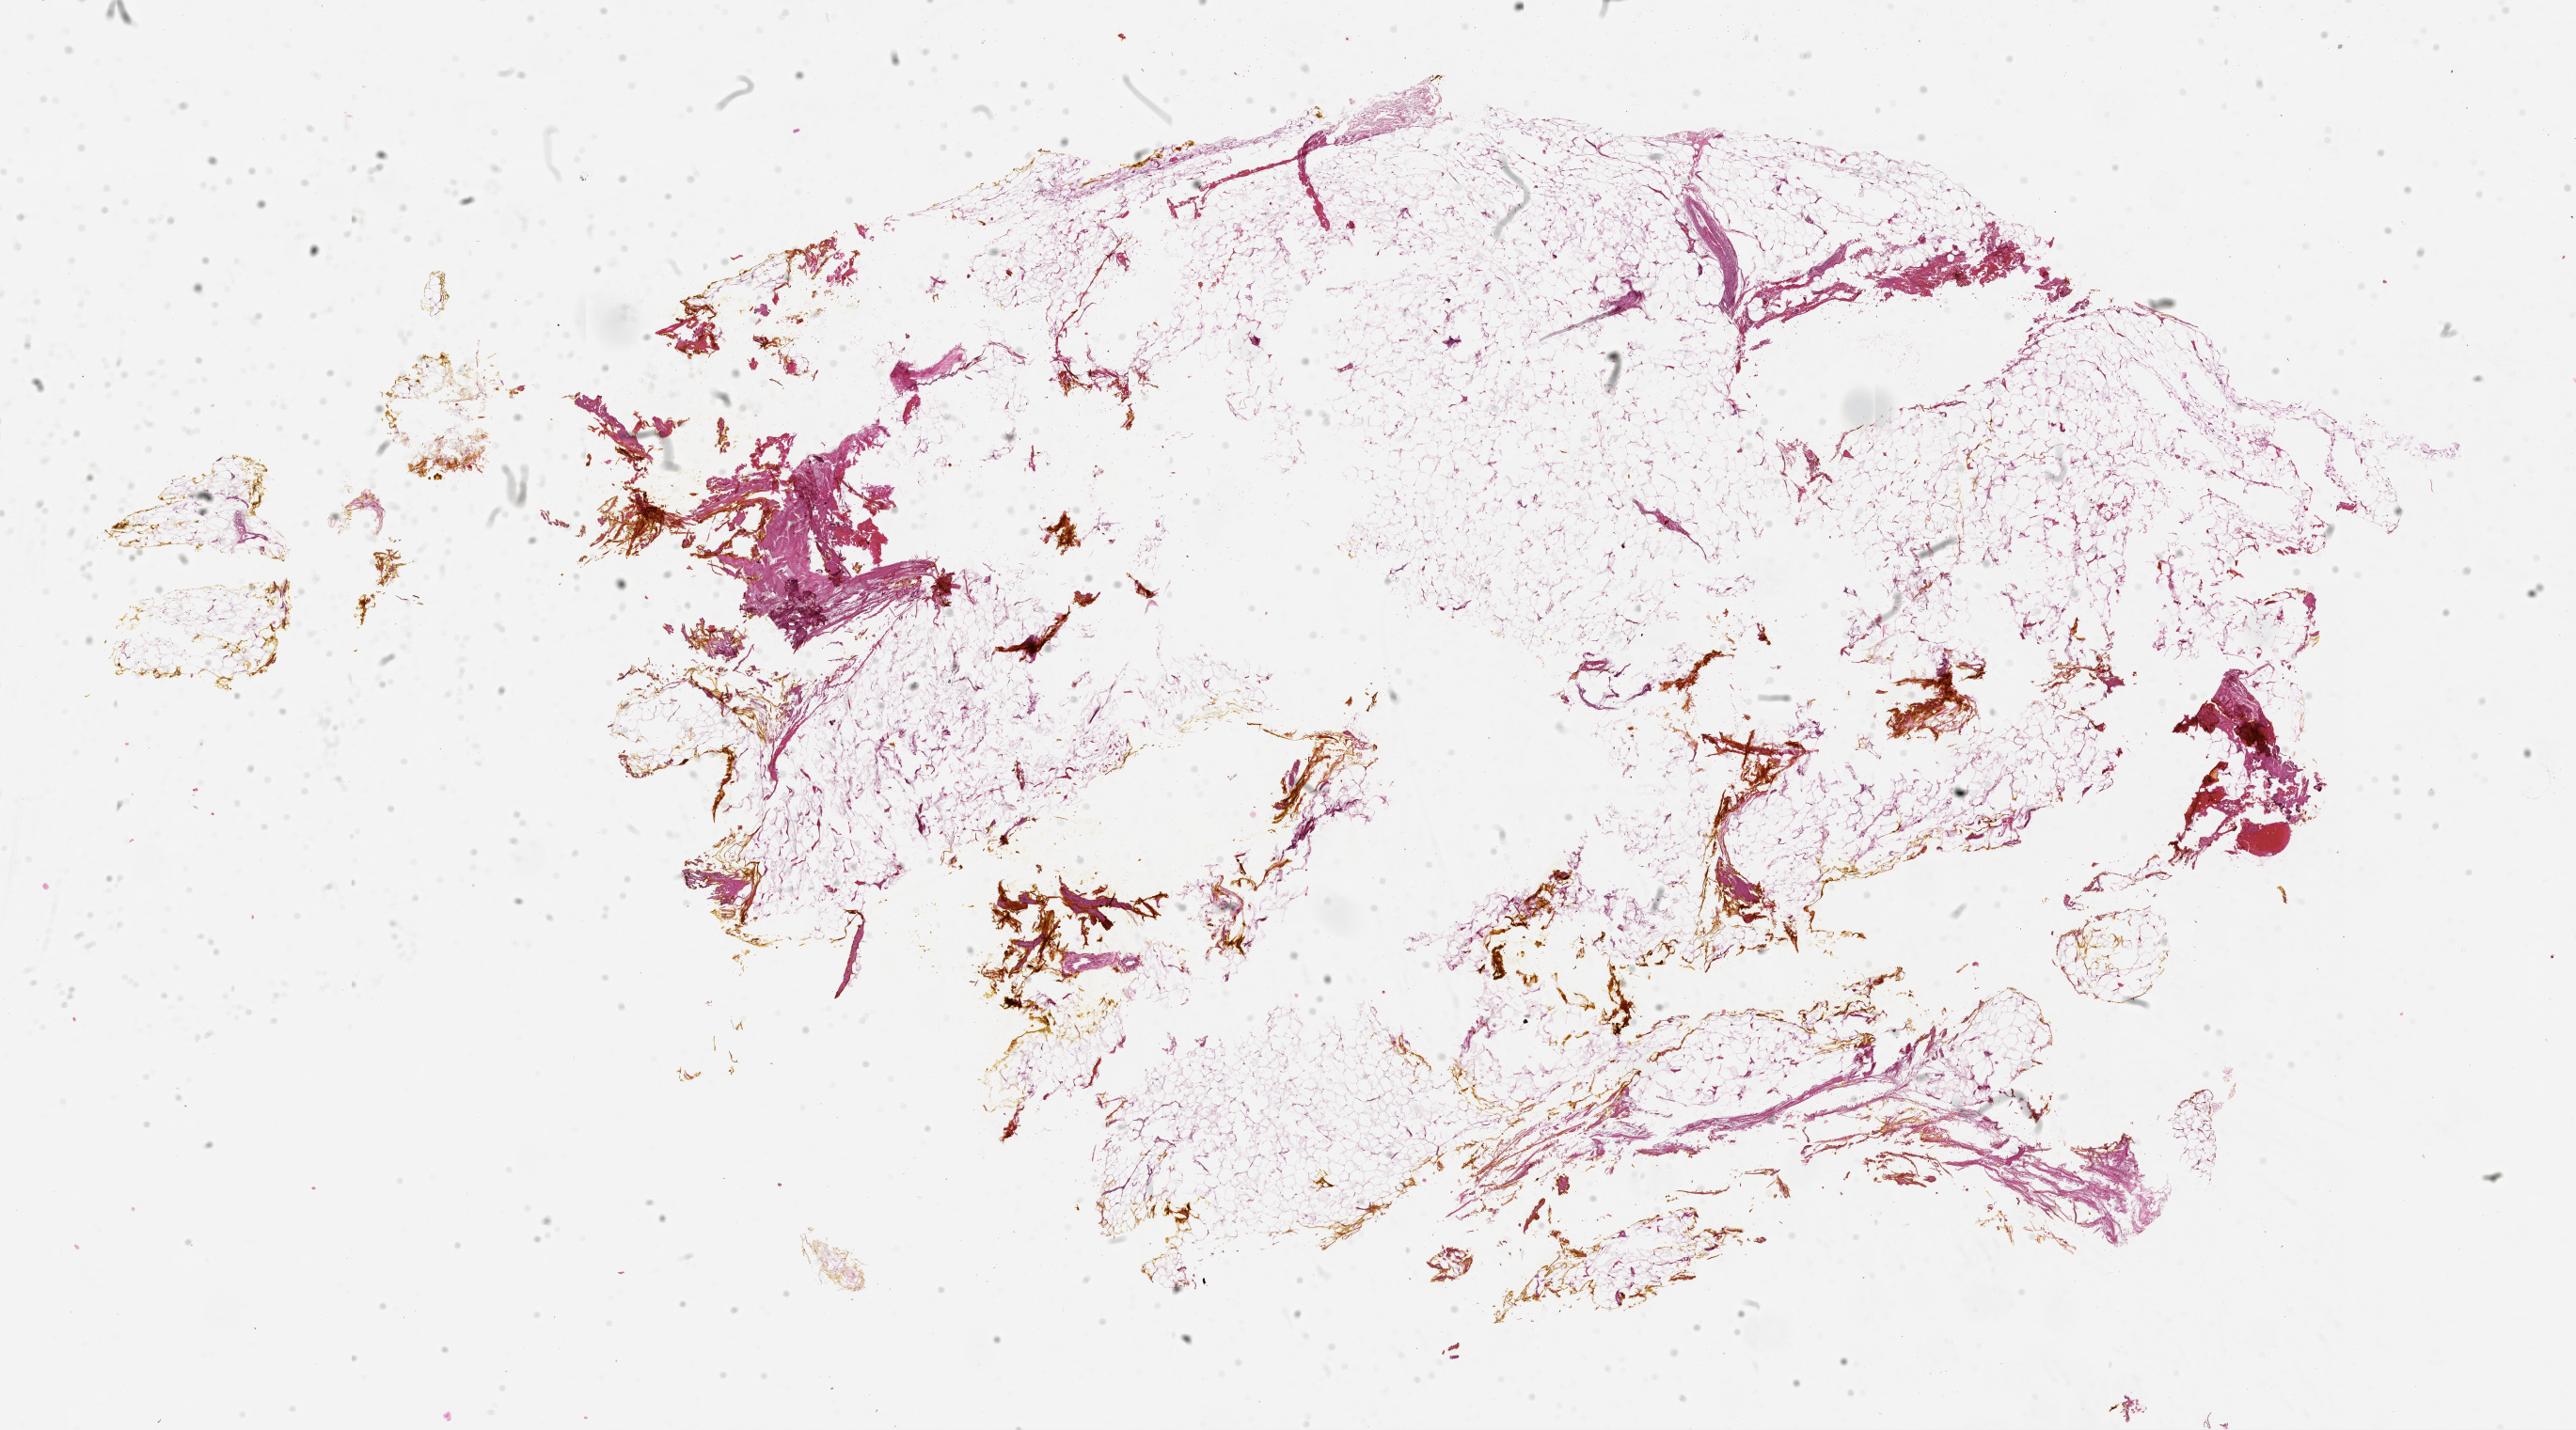
Digitized H&E tissue section (whole slide), low-resolution overview of the scanned area, about 22.0 x 12.2 mm (slide scanned at 20x).
* patient diagnosis (cohort enrolment): sarcoma (site not recorded at cohort level)